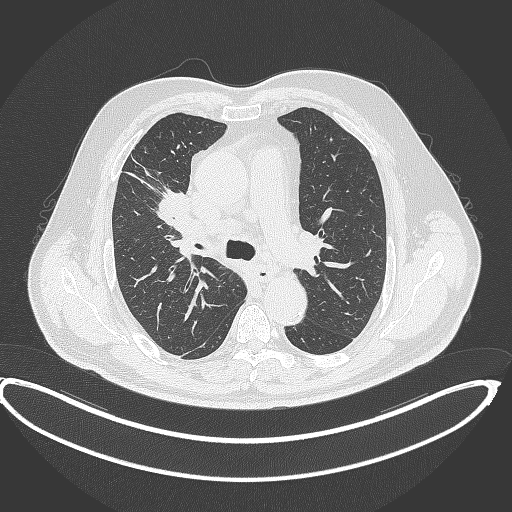
Chest CT, one axial slice. Slice 269 of 390 in the series (ordered by position). 120 kVp. Lung window (W 1500 / L -600 HU). 1 mm slice thickness. 512 × 512 image matrix, field of view 448 × 448 mm. Male patient, age 62 years. Case-level facts recorded for this patient, not image findings: clinical TNM (as recorded): T1c N3 M1c.
Structures marked on this image (rectangle marked by the reading radiologist):
- lung tumour (recorded histology: adenocarcinoma): box from (x=154, y=184) to (x=194, y=235) px